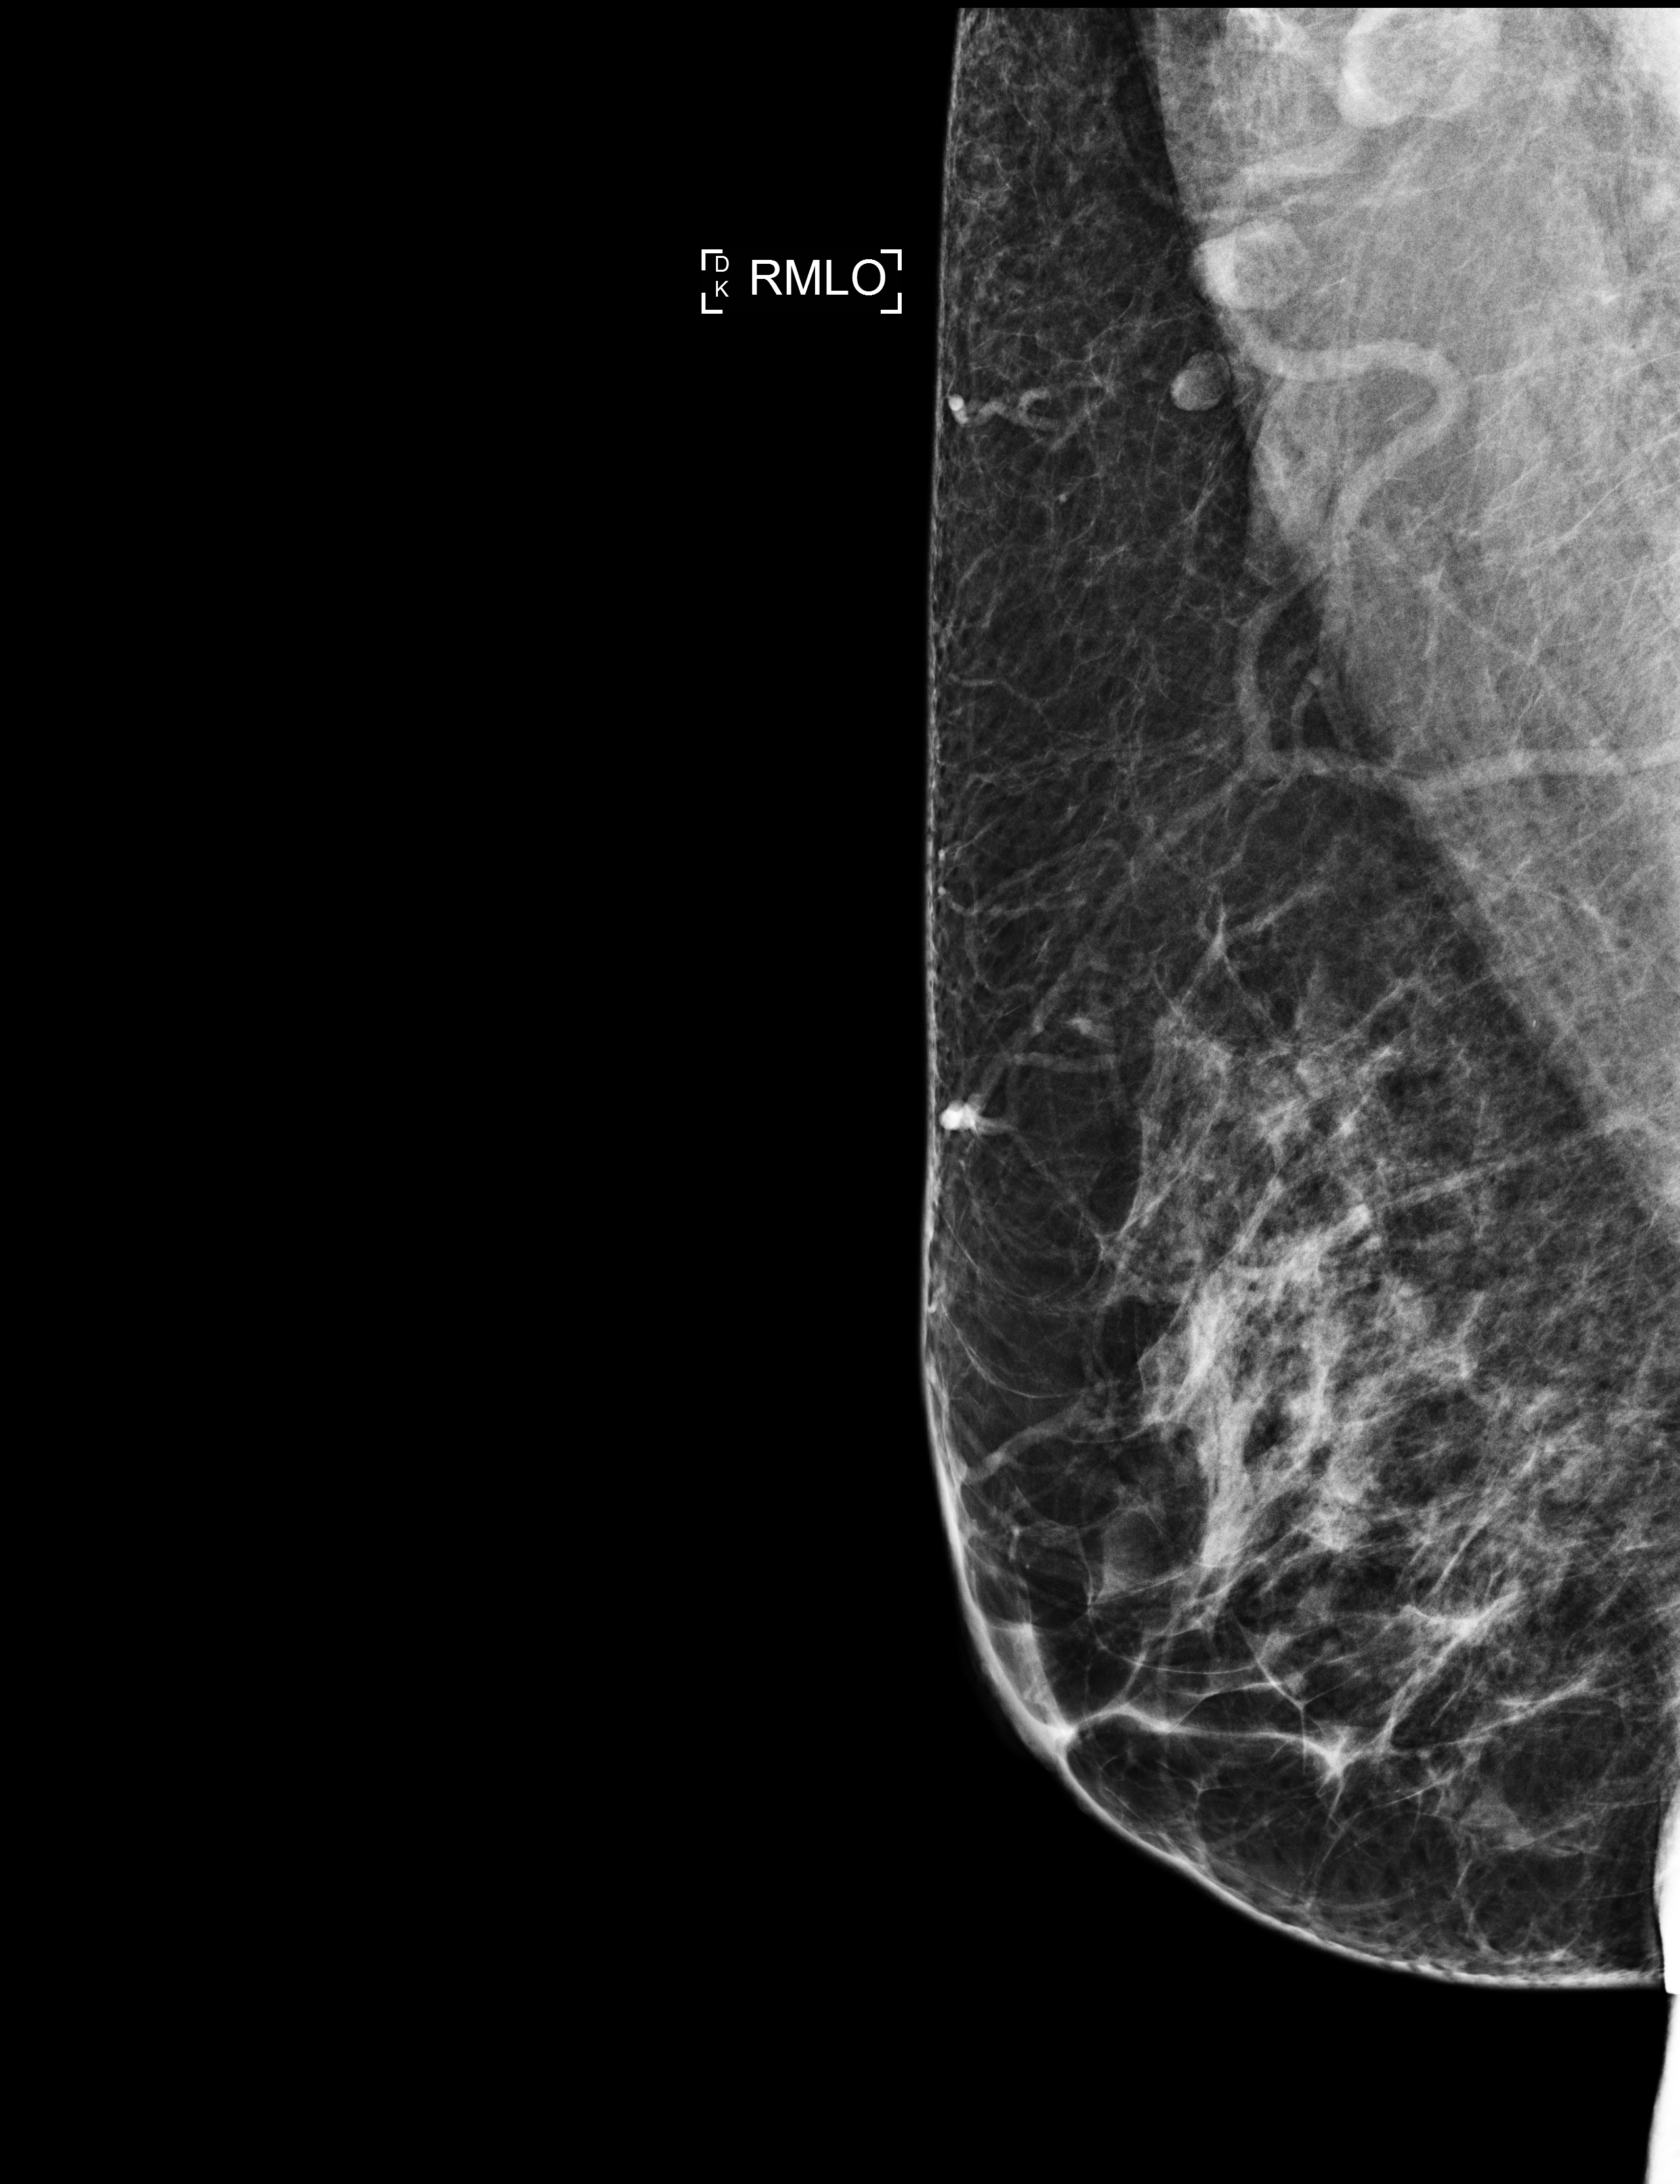
Screening examination, compressed breast thickness 69 mm. Patient aged 46 years (female).
Image type: full-field digital mammogram. Breast: right. Projection: medio-lateral oblique projection.